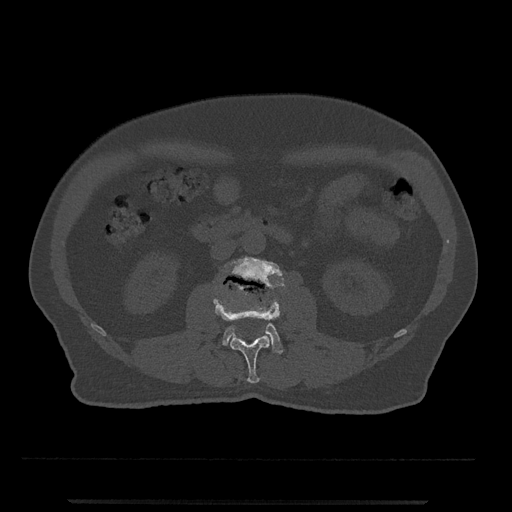
CT including the spine, one axial slice; slice 241 of 797 in the series (ordered by position); reconstruction kernel Br40s/3; 120 kVp; bone window (W 1800 / L 400 HU); 0.5 mm slice thickness; 512 × 512 image matrix, field of view 419 × 419 mm. Patient: male, 63 years. From the clinical record (not read from this slice): primary cancer: prostate.
Outlined on this slice (semi-automatically segmented with operator editing):
- L2 vertebra: bounding box <213,282,280,383> (left, top, right, bottom; pixels)
- L3 vertebra: <223,256,285,354>